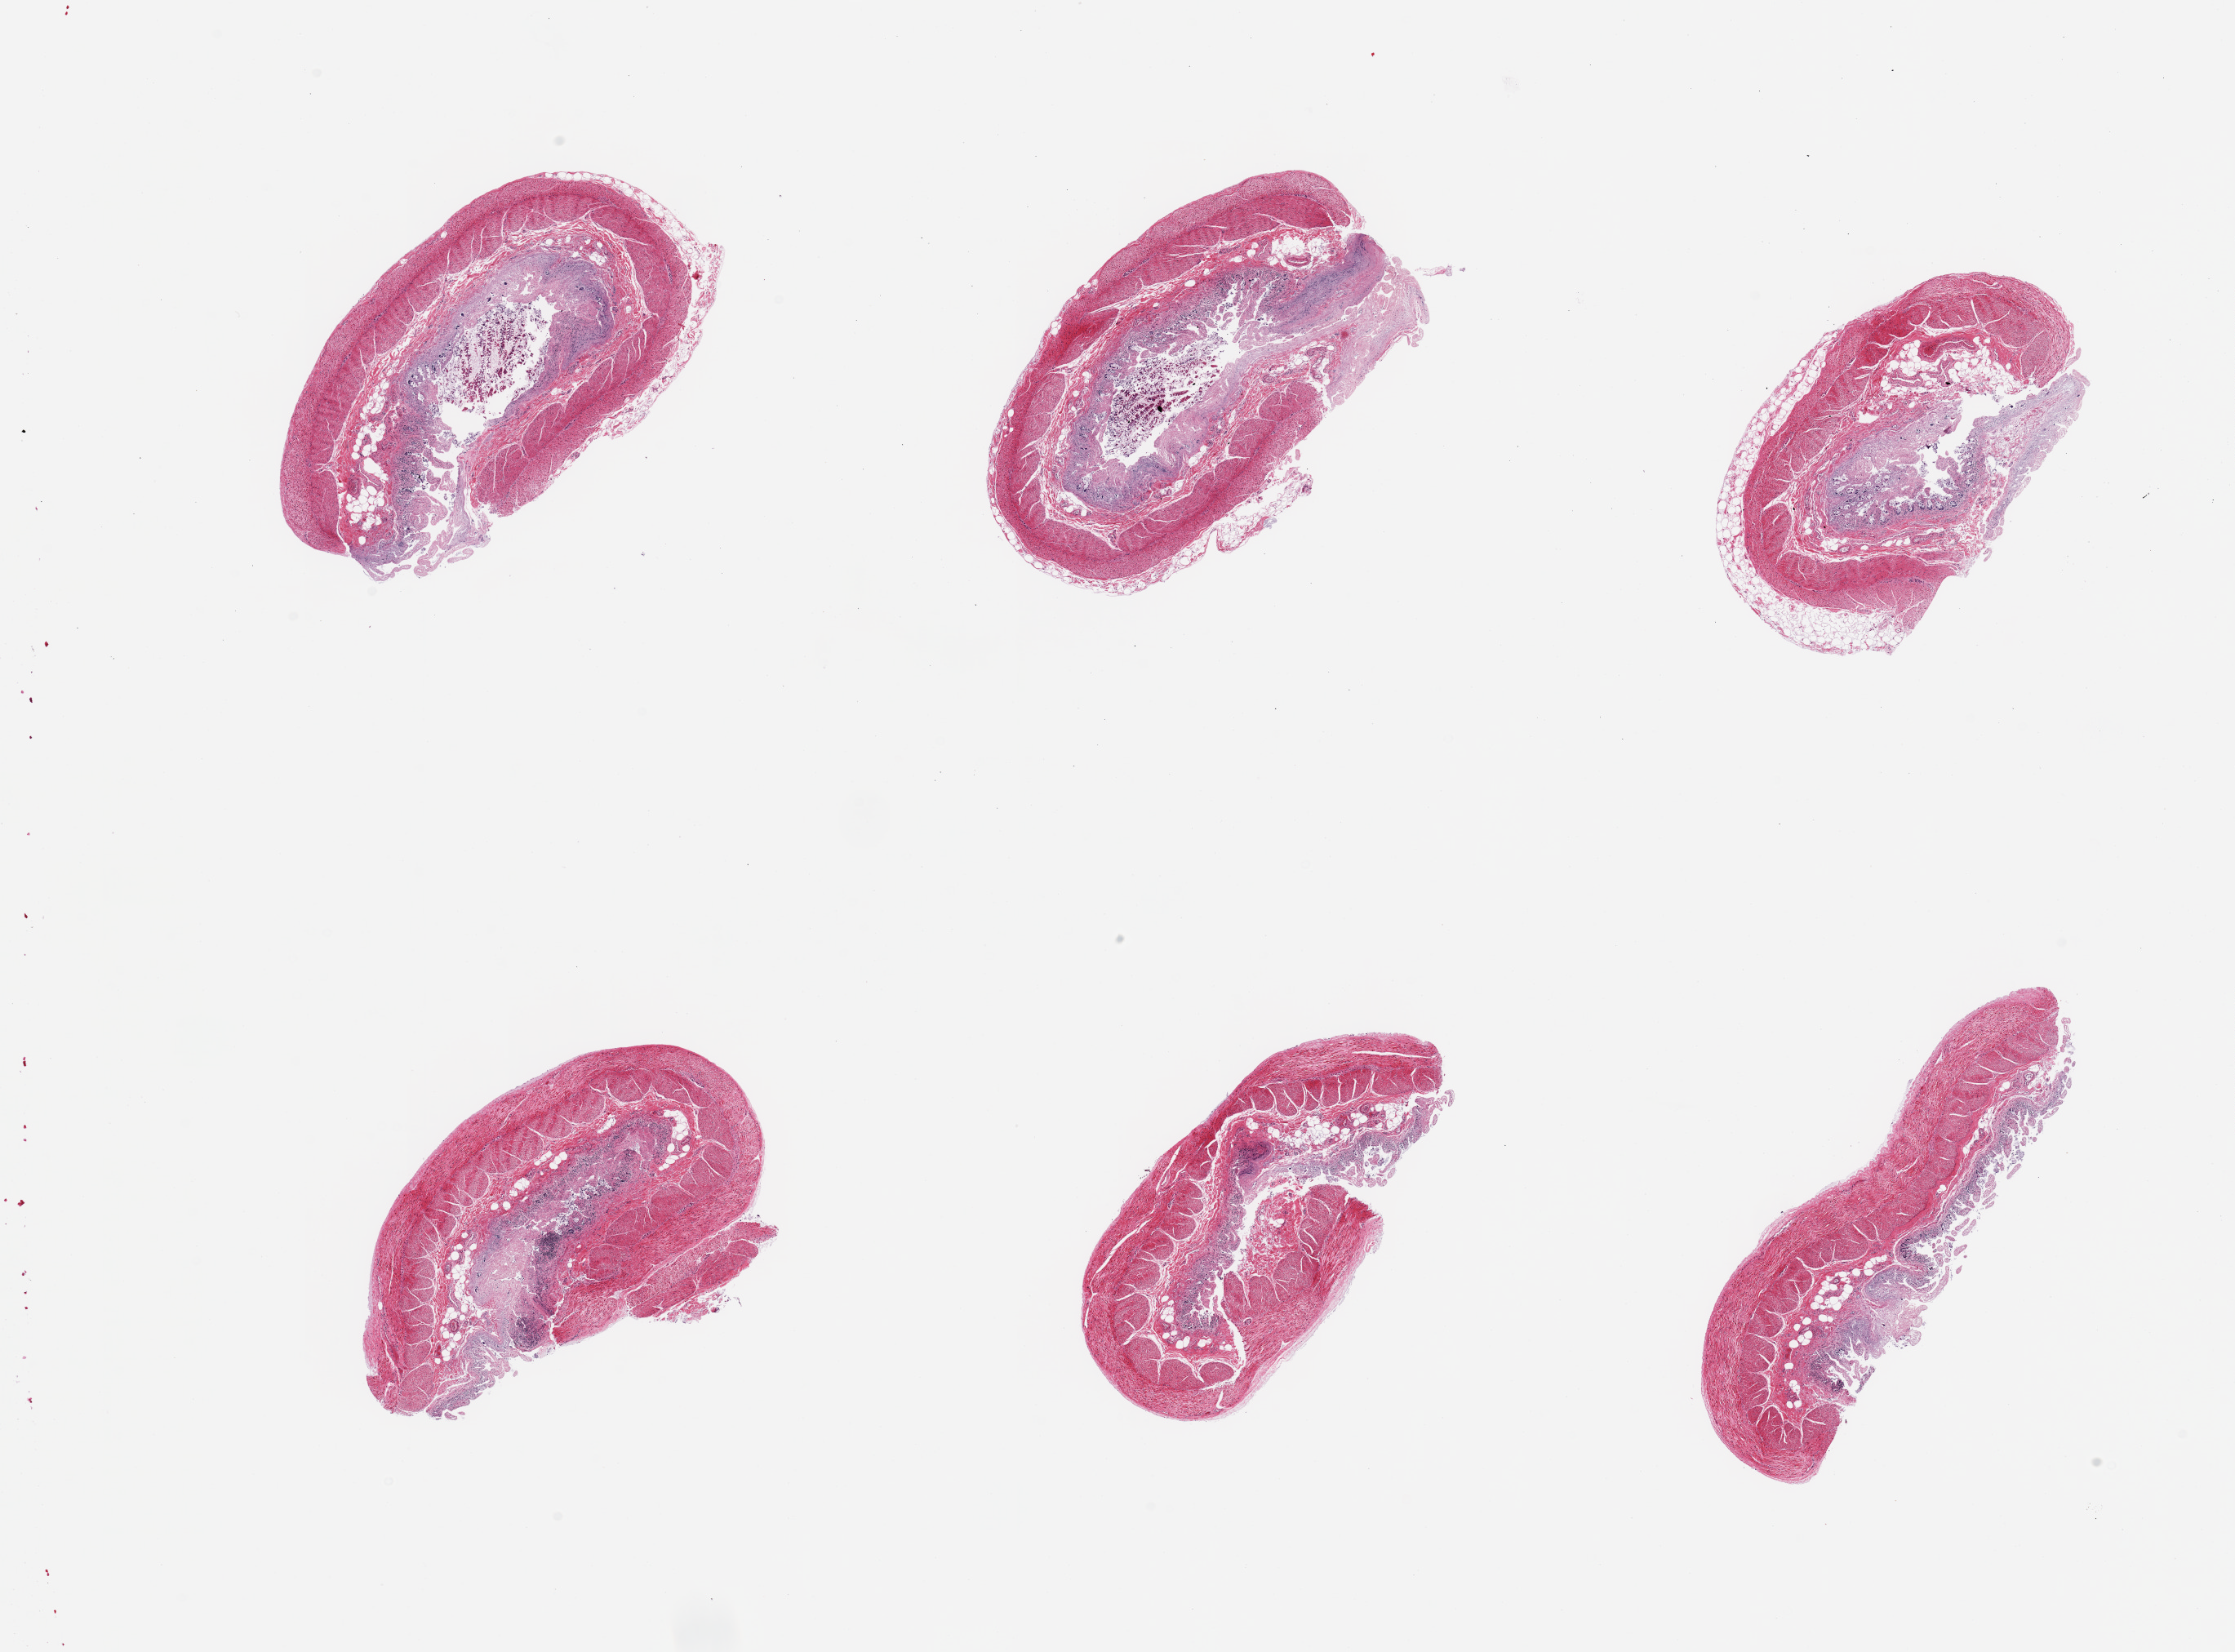
Whole-slide image, H&E stain, a low-resolution overview of the entire scanned area, about 21.7 x 16.0 mm (acquisition: 20x scan); PAXgene-fixed paraffin-embedded (PFPE) section; section of transverse colon (target tissue); donor tissue sample. Donor sex: female.
Review note (as recorded): 6 pieces, glandular mcuosa up to ~0.6mm; glandular elements totally sloughed, lamina propria only.